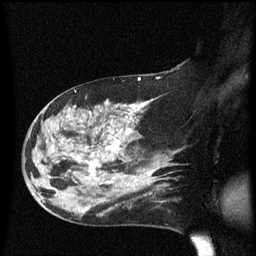
Breast MRI (dynamic contrast-enhanced), one sagittal slice. Position 35 of 60 along the scan axis. Dynamic contrast-enhanced series, image 2 of 3 at this slice position (ordered by acquisition). 1.5 T. TE 4.2 ms, TR 8.4 ms. 256 × 256 image matrix. Patient: female, 47 years.
Structures marked on this image (semi-automatic segmentation, software-assisted and operator-edited):
- analysis volume of interest (the breast-tissue region the enhancement analysis was run in; not a lesion): bounding box <24,97,149,206> (left, top, right, bottom; pixels)
- tumour enhancement mask (voxels above the 70 % enhancement threshold inside the analysis volume of interest): <56,102,149,197>